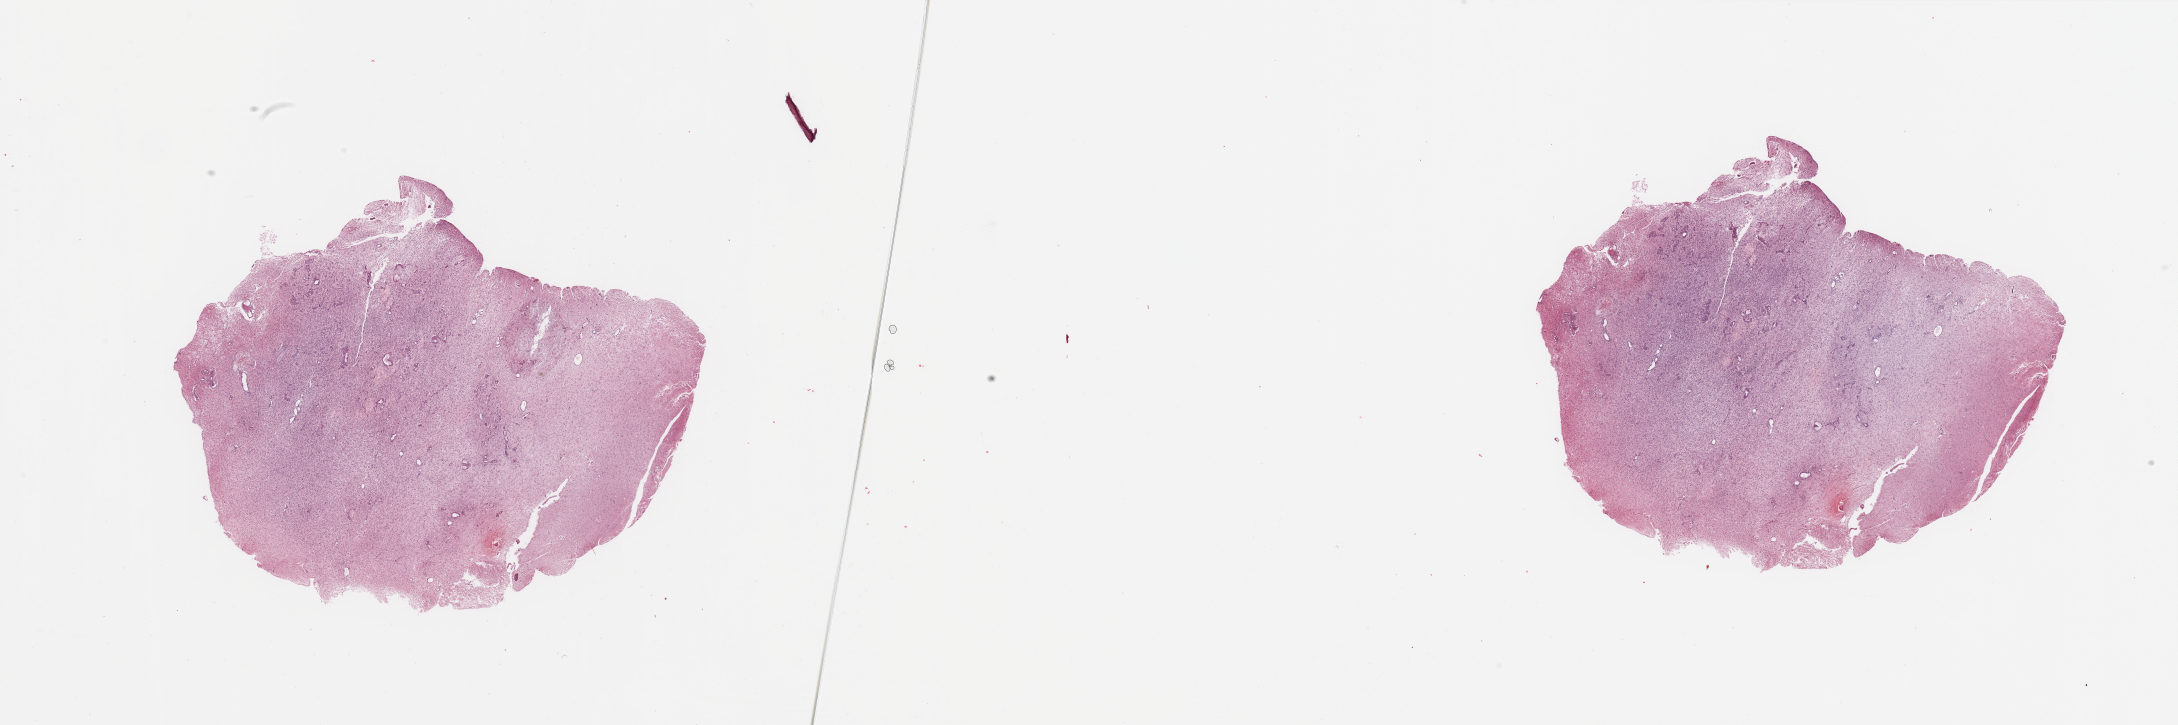
Digitized Hematoxylin and eosin (H&E) stained tissue section (whole slide) — low-resolution overview of the scanned area, about 34.5 x 11.5 mm (slide scanned at 20x). Tumour tissue sample, sampled site: brain. 84-year-old female patient. Composition of this section per pathologist review: tumour nuclei 90%, necrosis 5%.
Histologic diagnosis: Glioblastoma. Primary tumour site (as recorded): parietal lobe.